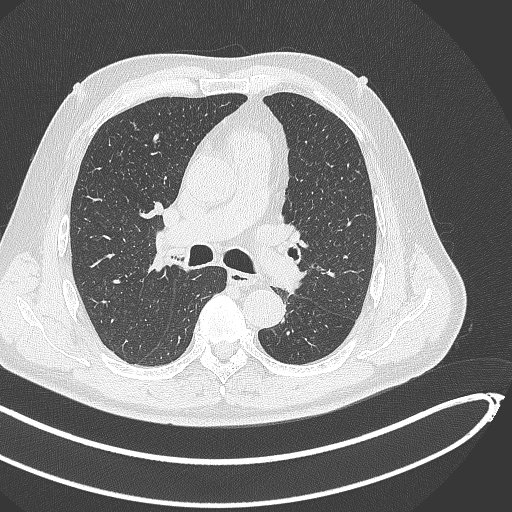
Chest CT, one axial slice. Reconstruction kernel B70f. 120 kVp. Lung window (W 1500 / L -600 HU). 1 mm slice thickness. 512 × 512 image matrix. Male patient, age 64 years. From the clinical record (not read from this slice): clinical TNM (as recorded): T1c N0 M0; histopathological grade: G2.
Outlined on this slice (rectangle marked by the reading radiologist):
- lung tumour (recorded histology: squamous cell carcinoma): bounding box <266,266,310,295> (left, top, right, bottom; pixels)